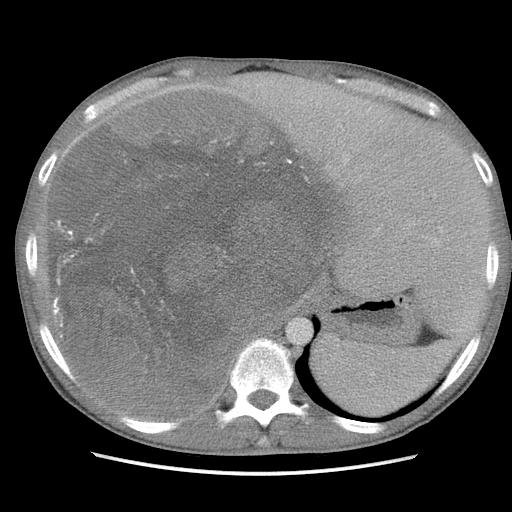
Contrast-enhanced abdominal CT, one axial slice; slice 82 of 115 in the series (ordered by position); soft-tissue window (W 400 / L 40 HU); 5 mm slice thickness; 512 × 512 image matrix. Male patient. From the clinical record (not read from this slice): diagnosis: adrenocortical carcinoma; tumour side: right adrenal; Ki-67 index: 13 %; stage (as recorded): 3.
Outlined on this slice (semi-automatically segmented with operator editing):
- mass: bounding box (x1, y1, x2, y2) in pixels: (56, 98, 331, 415)